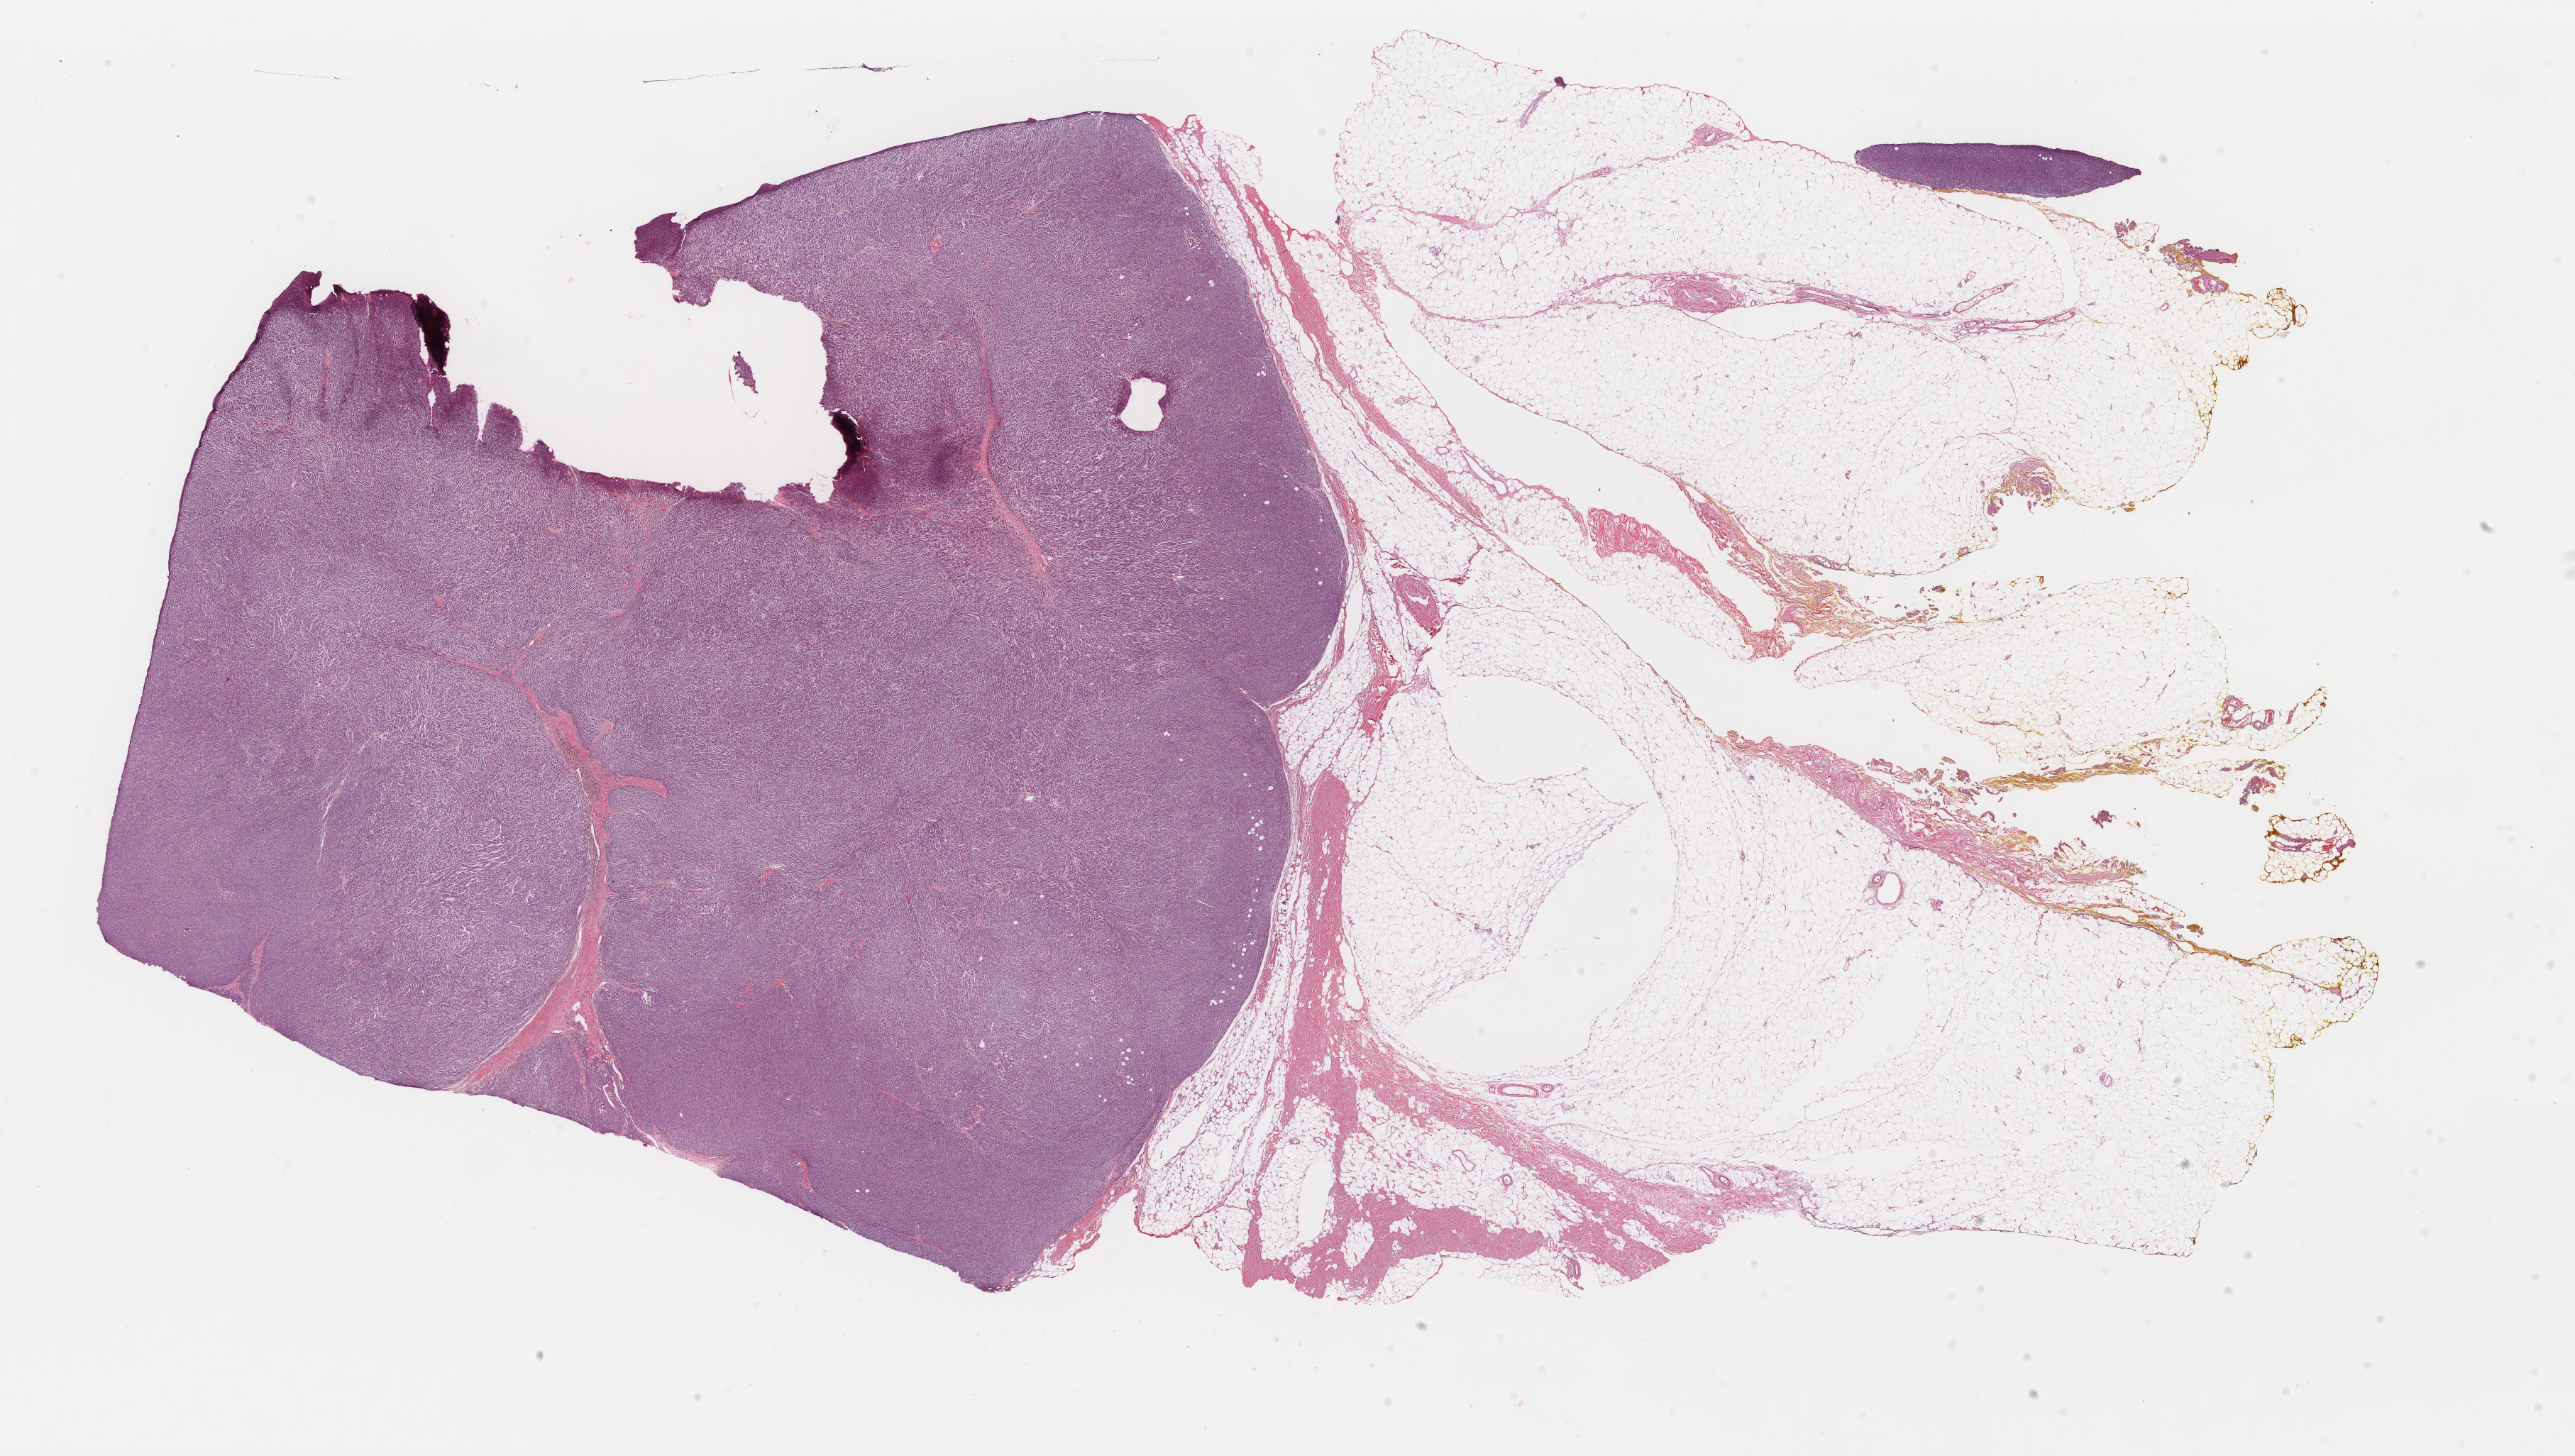
Digitized H&E tissue section (whole slide), shown as a low-resolution overview of the whole scanned area (about 28.8 x 16.3 mm, from a 40x scan). Formalin-fixed paraffin-embedded (FFPE) diagnostic section. Skin, primary tumour sample. Patient: male, age at initial diagnosis 60 years.
Pathologic diagnosis: Malignant melanoma, NOS.